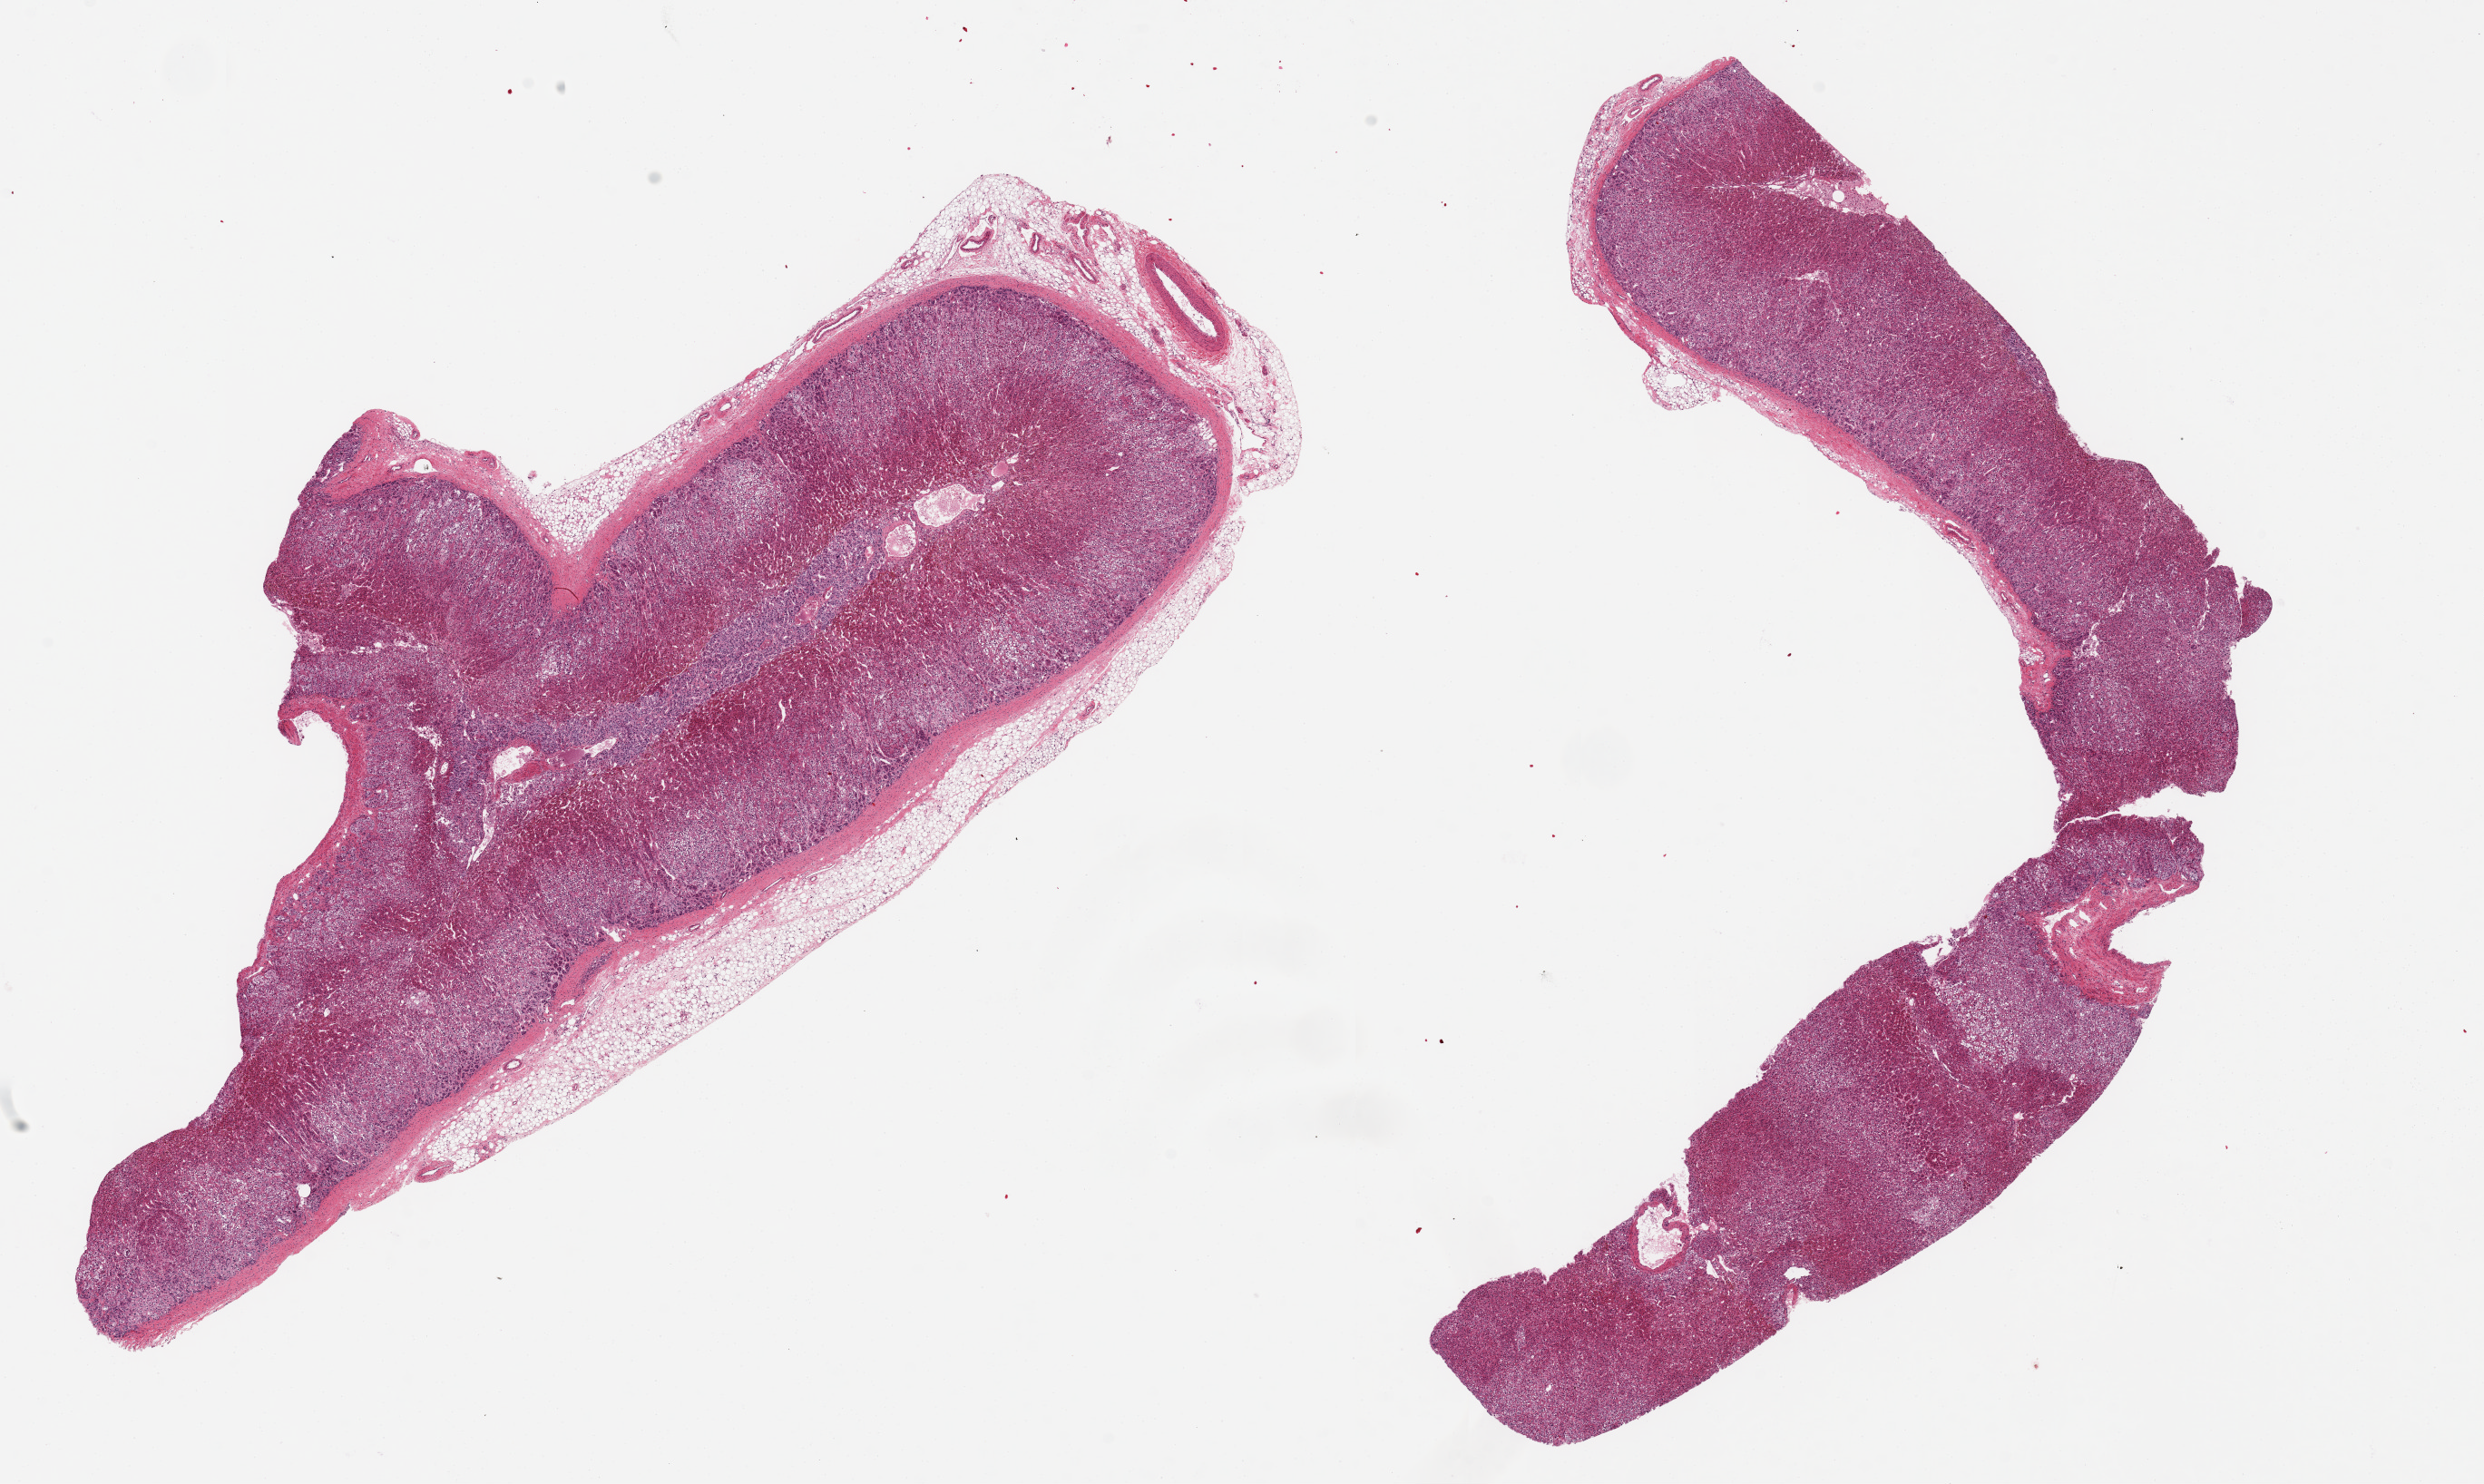
Digitized haematoxylin and eosin-stained section, brightfield, shown as a low-resolution overview of the whole scanned area (about 21.7 x 12.9 mm), PAXgene-fixed, paraffin-embedded tissue, section of adrenal gland (target tissue), donor tissue sample. Donor sex: female.
* reviewer comment on this tissue sample: 2 pieces ~13x3mm, all layers of cortex seen; discontinuous rim of adherent fat up to ~0.7mm